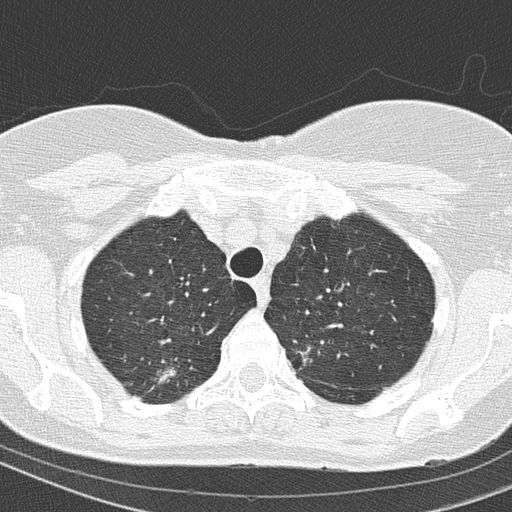
Low-dose screening chest CT, axial slice. Baseline annual screen. Lung window (W 1500 / L -600 HU). Lung (sharp) reconstruction kernel (B50f). Female, age 67 years at enrolment. Current smoker at enrolment.
Expert-annotated lung lesion, bounding box <137,350,196,403> (left, top, right, bottom; pixels). Screening reader's record for this exam (one nodule recorded; not confirmed to be the boxed lesion): non-calcified nodule or mass ≥4 mm, right upper lobe, 15 × 14 mm, spiculated (stellate) margins, soft tissue attenuation. Later outcome: lung cancer diagnosed 63 days after this screen — adenocarcinoma, NOS, right upper lobe, moderately differentiated (G2), stage IA (AJCC 6th edition), 14 mm at pathology.